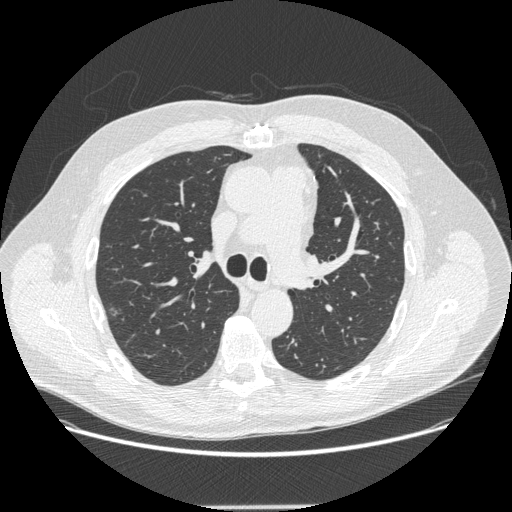
Axial slice from a low-dose chest CT screening exam; third annual screen; lung window (W 1500 / L -600 HU); standard (soft-tissue) reconstruction kernel (STANDARD); 120 kVp; slice 82 of 265 in the series; 512 × 512 image matrix. Male, age 62 years at enrolment.
• Lesion marked by an expert reader, bounding box <94,299,133,329> (left, top, right, bottom; pixels).
• Screening reader's record for this exam (one nodule recorded; not confirmed to be the boxed lesion): non-calcified nodule or mass ≥4 mm, right upper lobe, 12 × 11 mm, smooth margins, soft tissue attenuation, pre-existing on the prior screen: yes; interval growth: yes.
• Lung cancer was diagnosed 112 days after this screen: adenocarcinoma, NOS, right upper lobe, moderately differentiated (G2), stage IA (AJCC 6th edition), 12 mm at pathology.